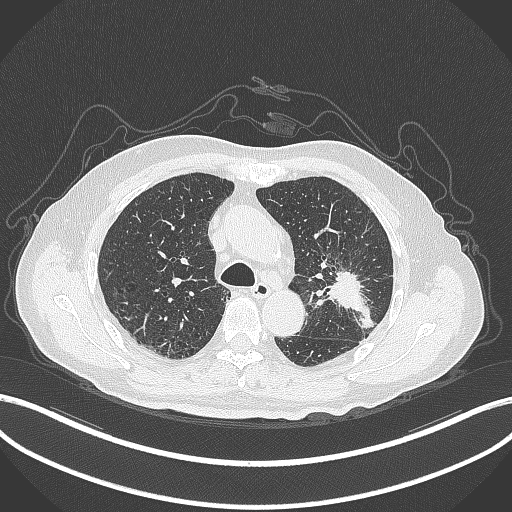
Chest CT, one axial slice. 120 kVp. Lung window (W 1500 / L -600 HU). 1 mm slice thickness. 512 × 512 image matrix, field of view 400 × 400 mm. Male patient, age 79 years. Case-level facts recorded for this patient, not image findings: clinical TNM (as recorded): T2a N1 M1.
Annotated regions visible in this slice (bounding box drawn by a radiologist):
- lung tumour (recorded histology: adenocarcinoma): box from (x=319, y=268) to (x=376, y=336) px